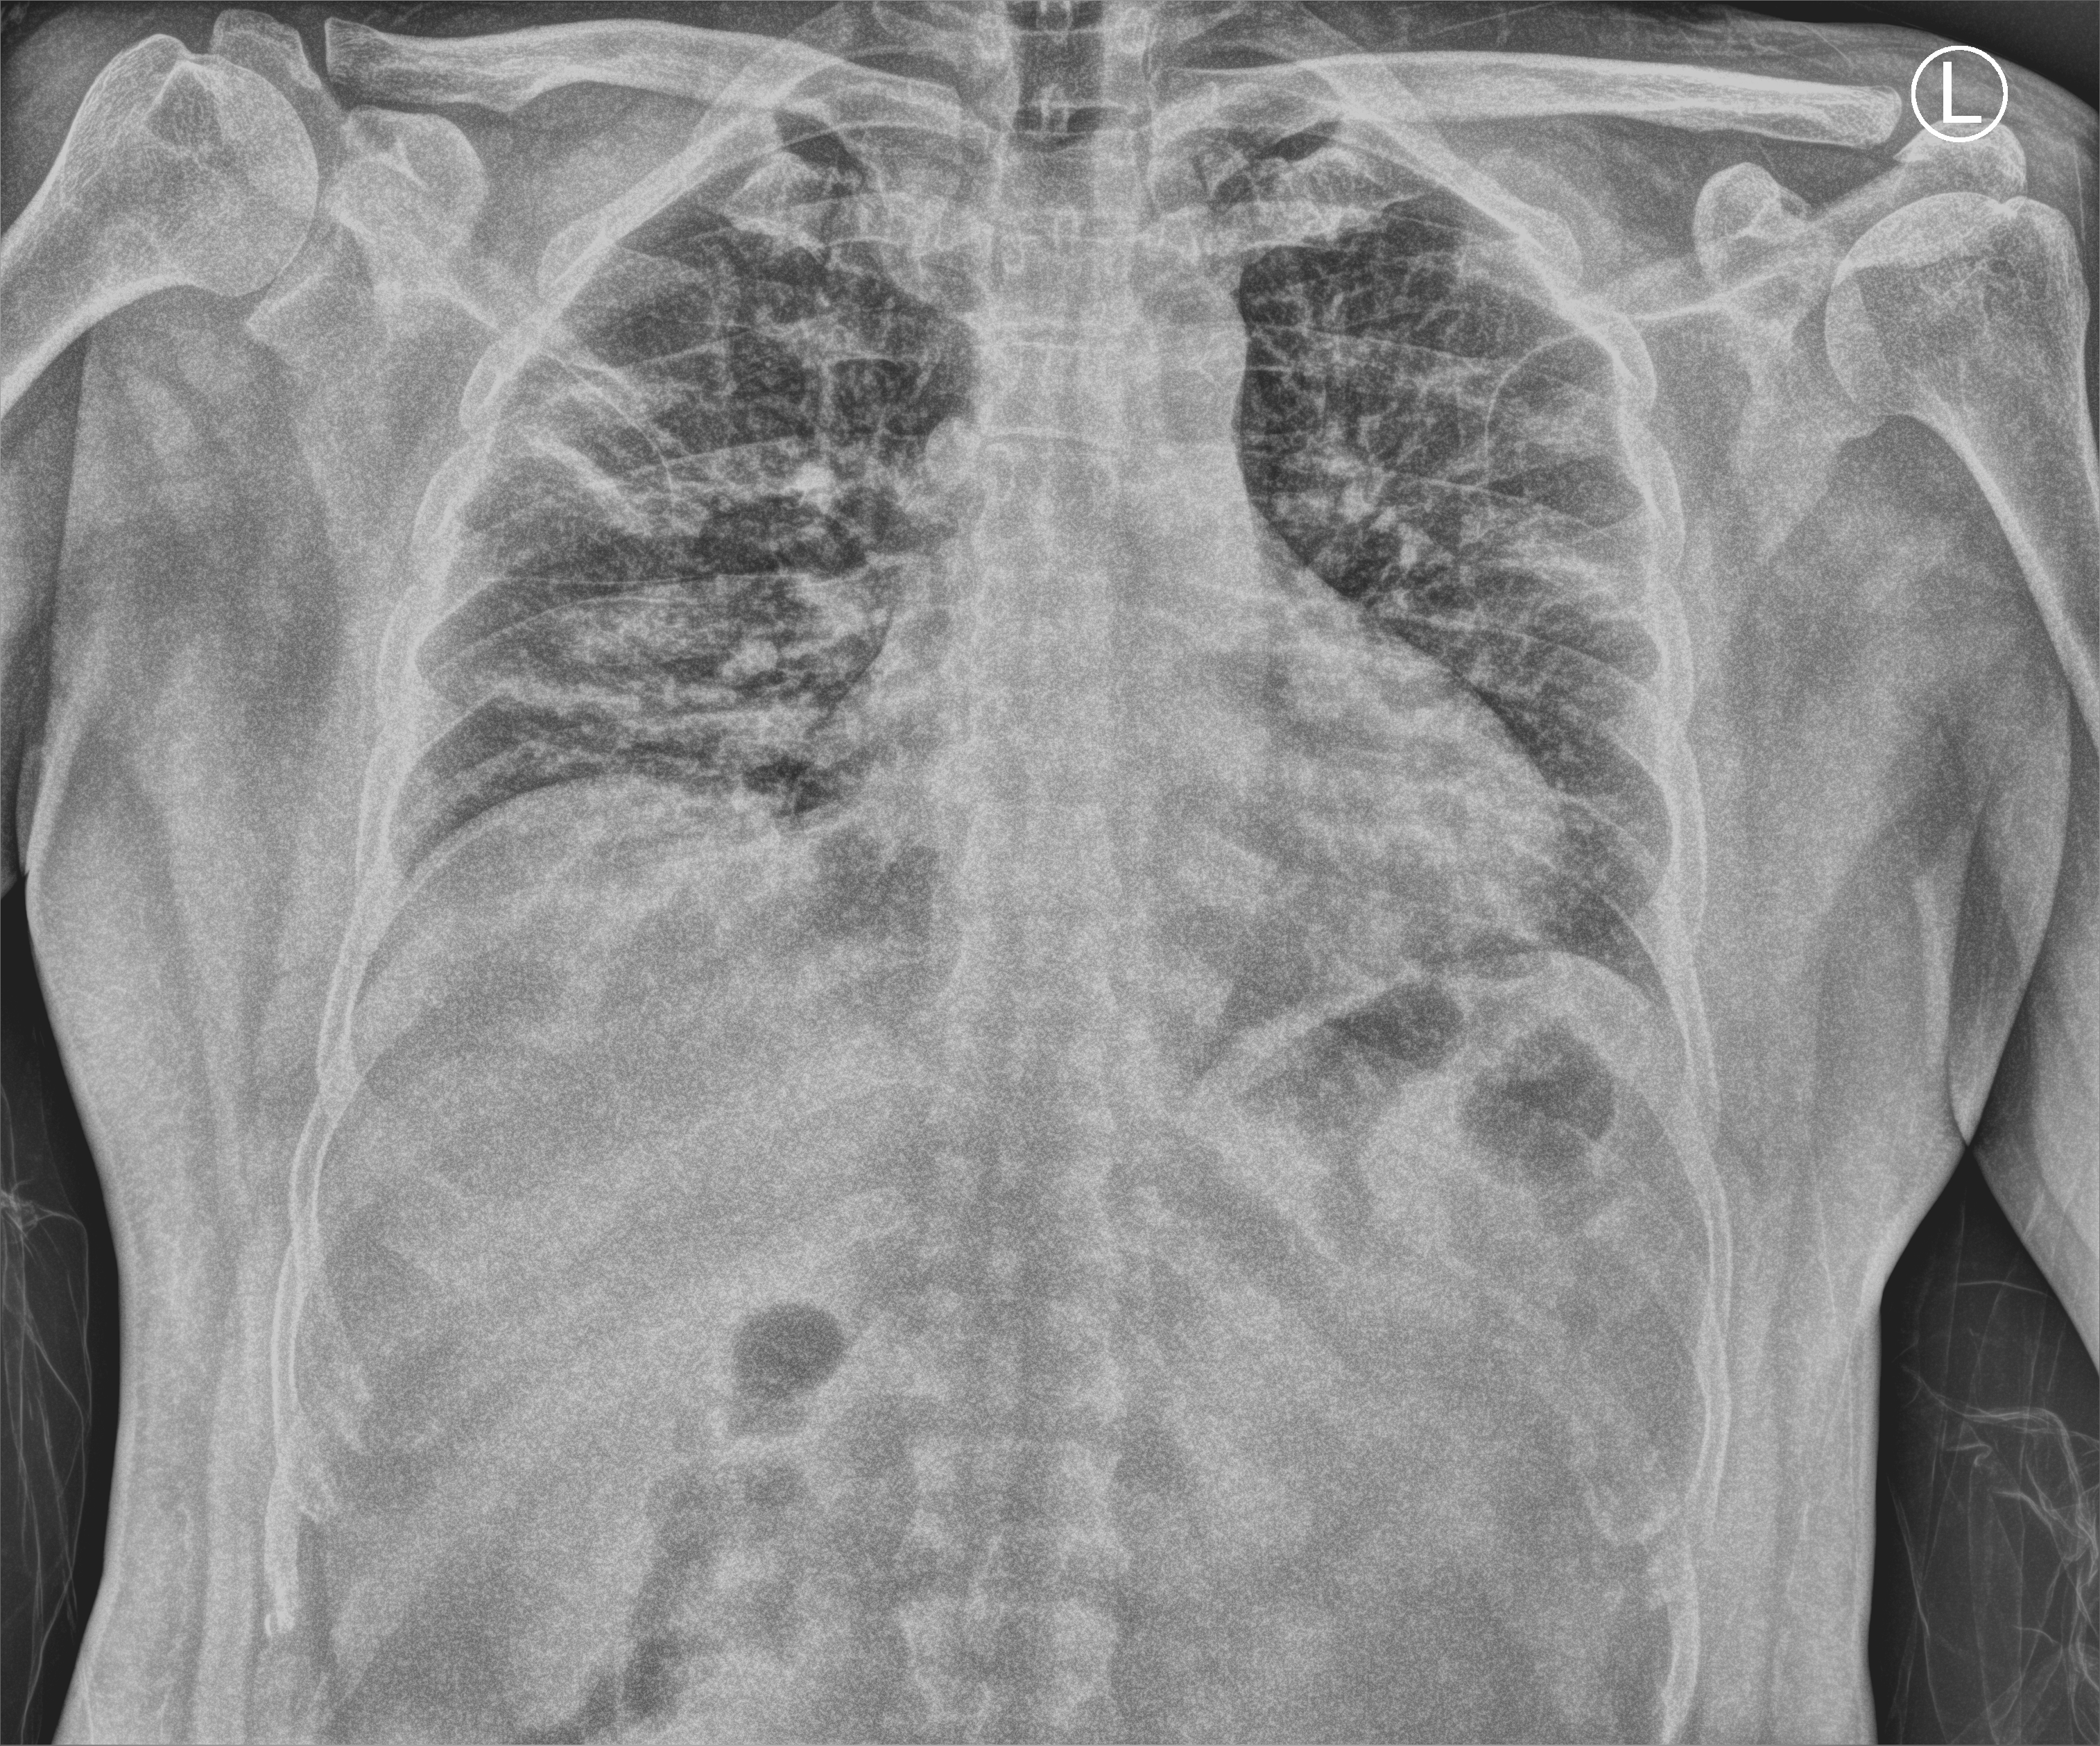
Bedside chest radiograph (computed radiography); anteroposterior (AP) projection. Male patient hospitalised with COVID-19, age 18–59 years.
From the hospital-stay record, not from the radiograph (when in the stay this image was taken is not recorded):
- admitted to intensive care during this hospital stay: no